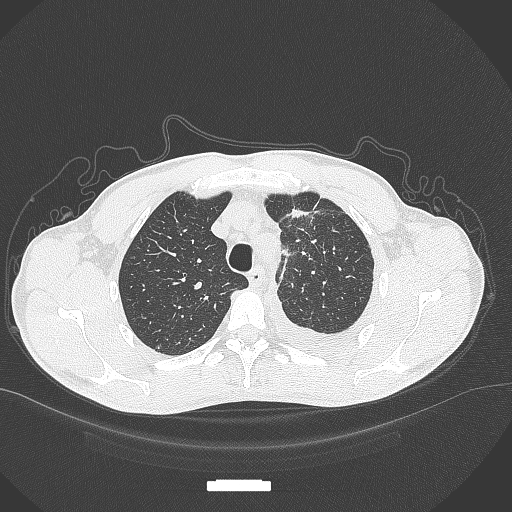
Chest CT, one axial slice; slice 273 of 371 in the series (ordered by position); lung window (W 1500 / L -600 HU); 1 mm slice thickness; 512 × 512 image matrix, field of view 400 × 400 mm. Patient: male, 49 years. From the clinical record (not read from this slice): clinical TNM (as recorded): T1c N1 M1.
Annotated regions visible in this slice (rectangle marked by the reading radiologist):
- lung tumour (recorded histology: adenocarcinoma): bounding box <278,203,319,228> (left, top, right, bottom; pixels)